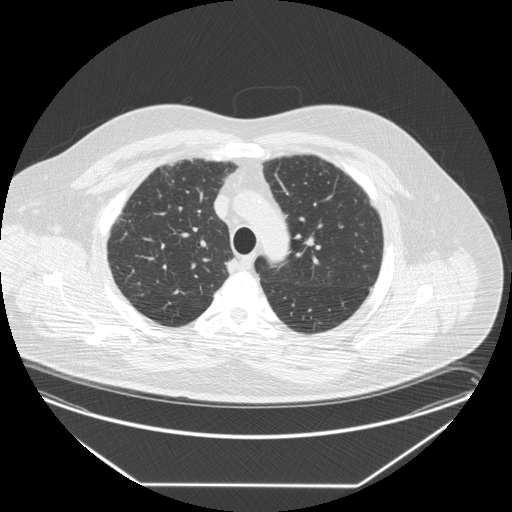
Low-dose screening chest CT, one axial slice. Position 205 of 258 along the scan axis. 120 kVp. Lung window (W 1500 / L -600 HU). 2.5 mm slice thickness. 512 × 512 image matrix.
Outlined on this slice (outlined manually by an expert reader):
- lesion 1 (tumor, upper lobe of right lung): bounding box <225,258,237,274> (left, top, right, bottom; pixels)